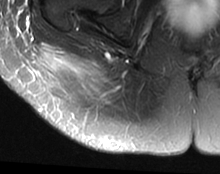
MRI of an extremity soft-tissue mass, one axial slice; slice 14 of 63 in the series (ordered by position); T2-weighted fat-saturated; MR volume resampled by the dataset authors to the PET/CT grid (not the native acquisition matrix); 3.27 mm slice thickness; 220 × 174 image matrix, field of view 215 × 170 mm. Female patient. From the clinical record (not read from this slice): histological type: spindle cell suggestive of myxofibrosarcoma; grade: intermediate; site of the primary tumour: right buttock.
Annotated regions visible in this slice (expert contour drawn on MRI and transferred to this co-registered scan by the dataset authors):
- gross tumour volume (mass): bounding box <40,45,112,103> (left, top, right, bottom; pixels)